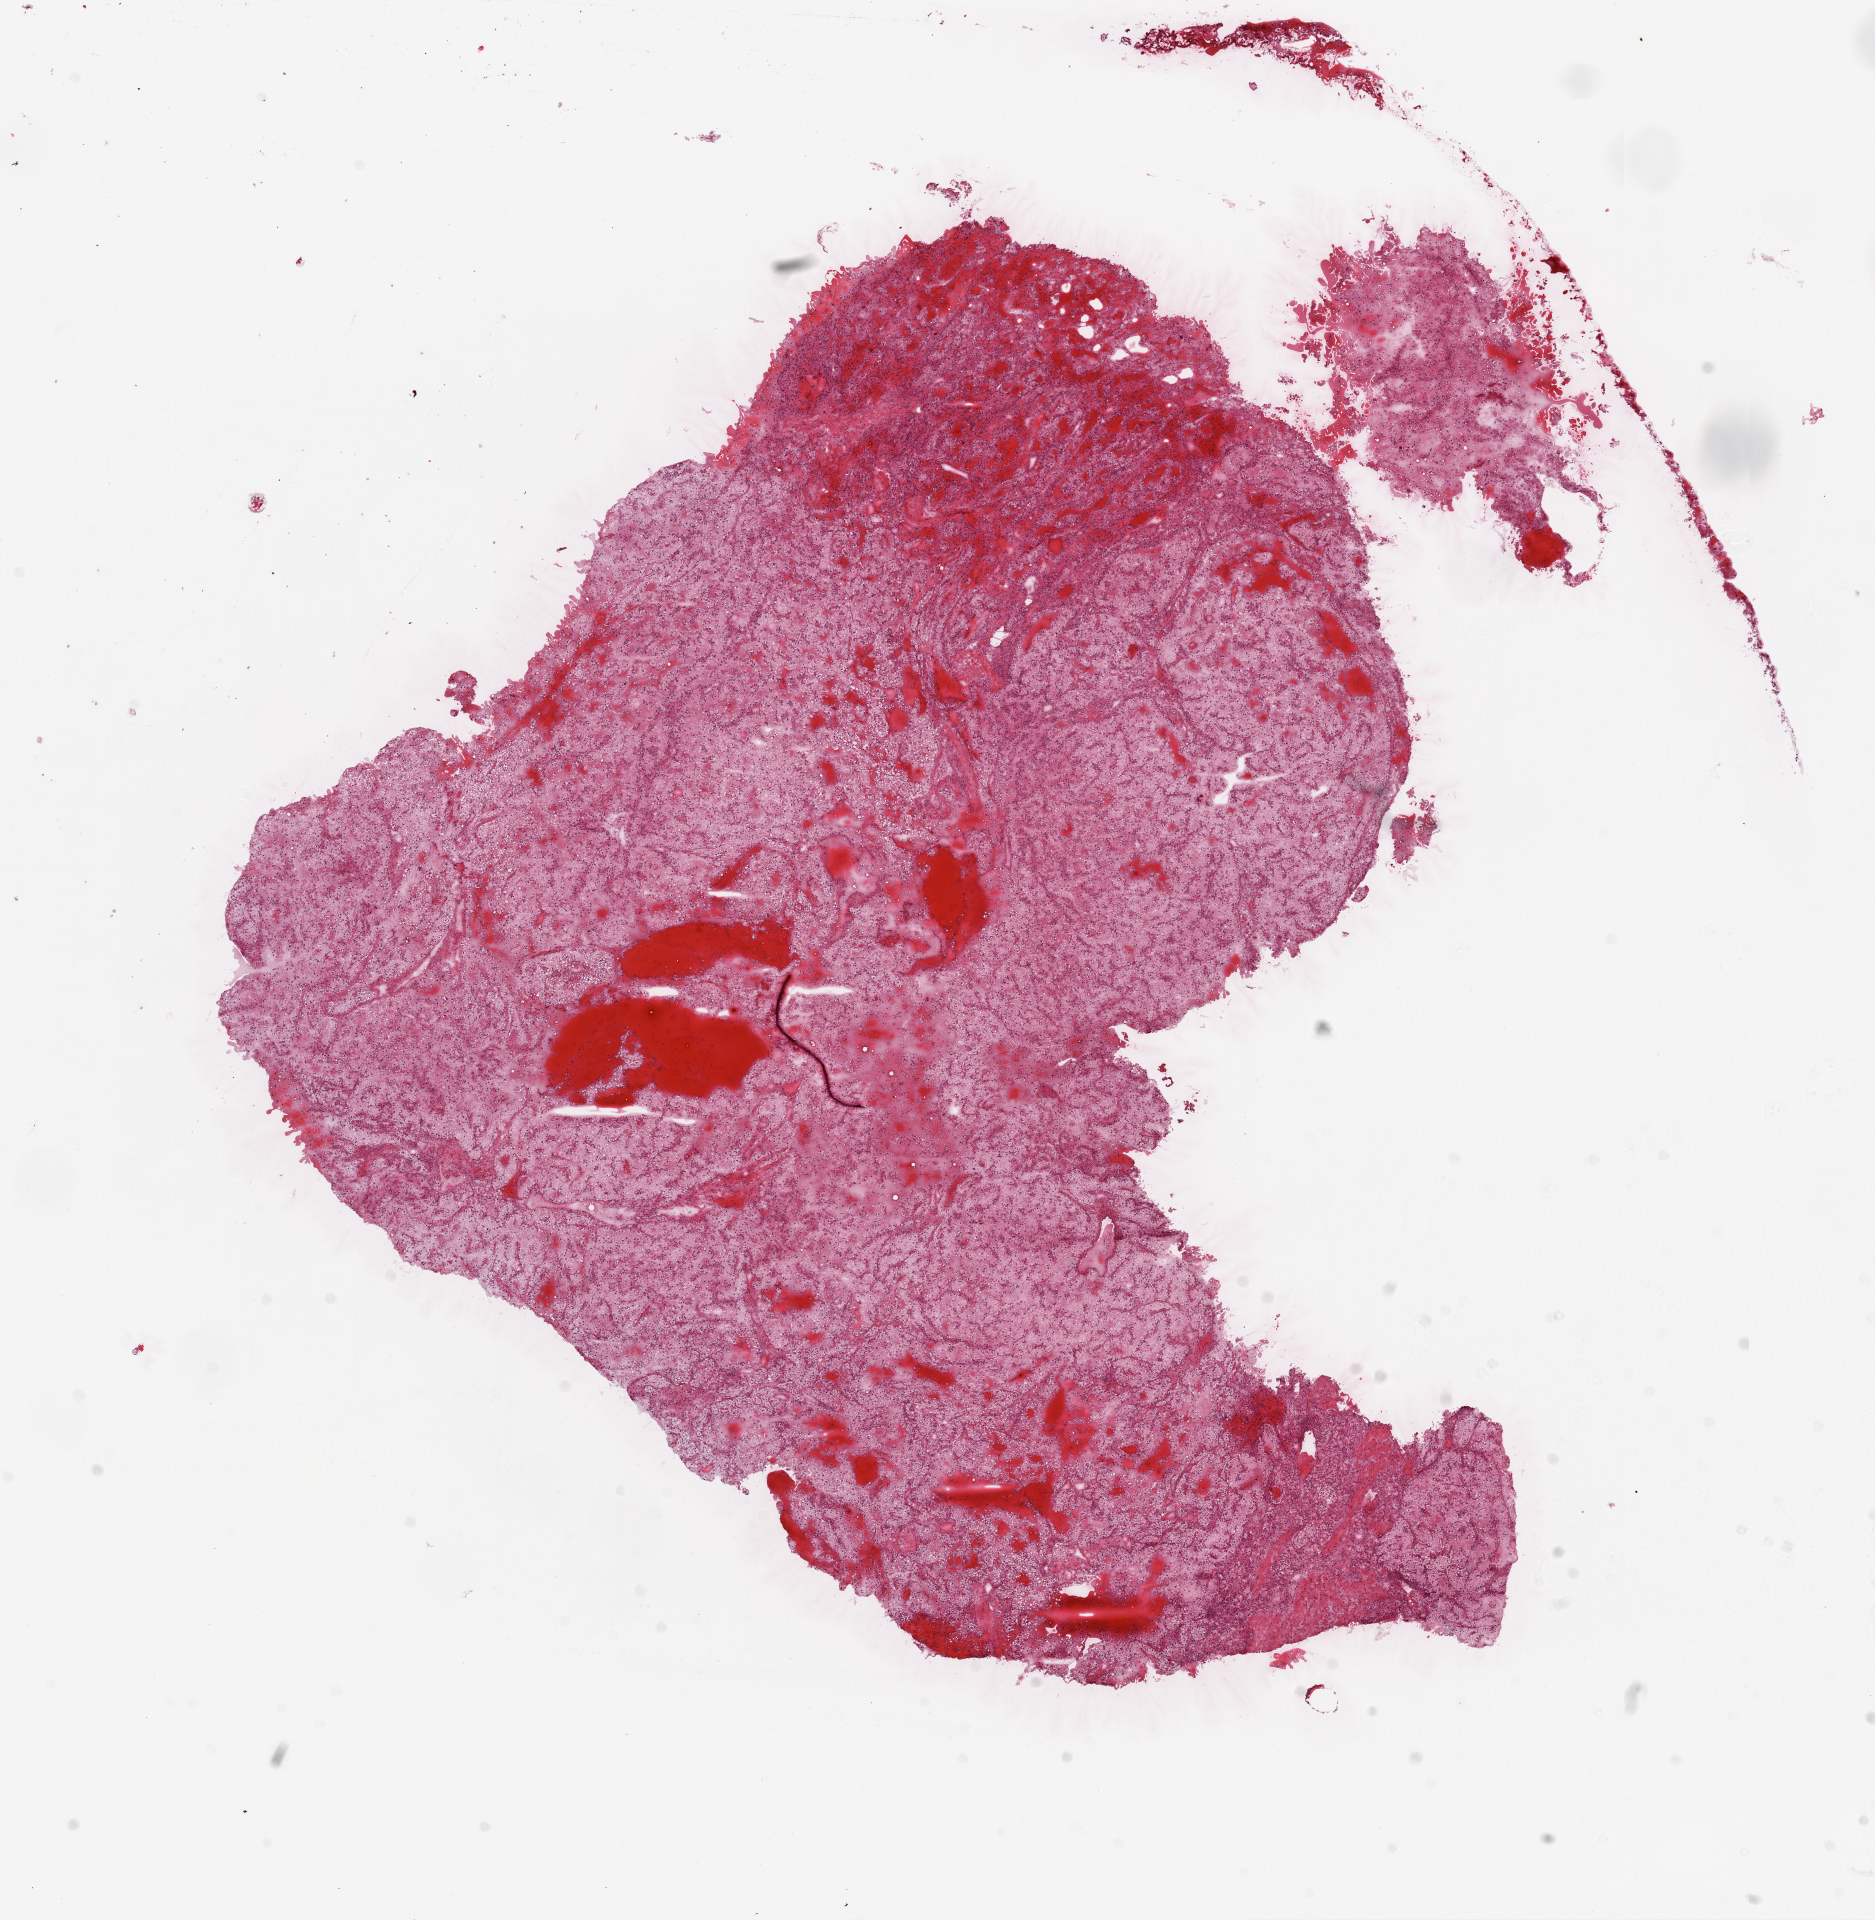
Digitized Hematoxylin and eosin (H&E) stained tissue section (whole slide), shown as a low-resolution overview of the whole scanned area (about 15.0 x 15.4 mm, acquisition: 20x scan); frozen section from the top of the tissue portion; sample: primary tumour, kidney. Male patient; age at initial diagnosis 34 years.
Diagnosis: Clear cell adenocarcinoma, NOS.